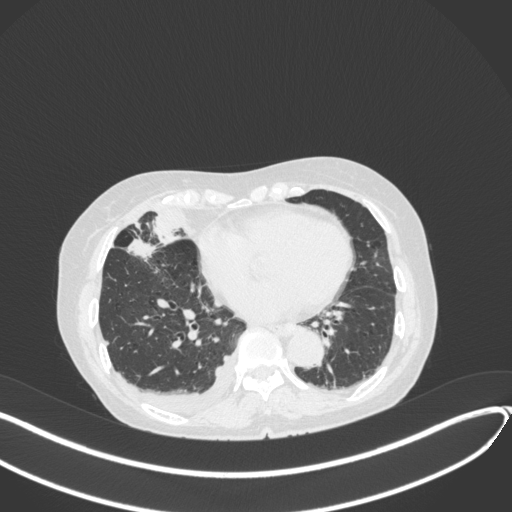
Chest CT, one axial slice. Position 145 of 418 along the scan axis. Lung window (W 1500 / L -600 HU). 512 × 512 image matrix, field of view 400 × 400 mm. Patient: female, 75 years. Case-level facts recorded for this patient, not image findings: clinical TNM (as recorded): T2a N3 M0.
Outlined on this slice (rectangle marked by the reading radiologist):
- lung tumour (recorded histology: adenocarcinoma): box from (x=123, y=236) to (x=160, y=265) px